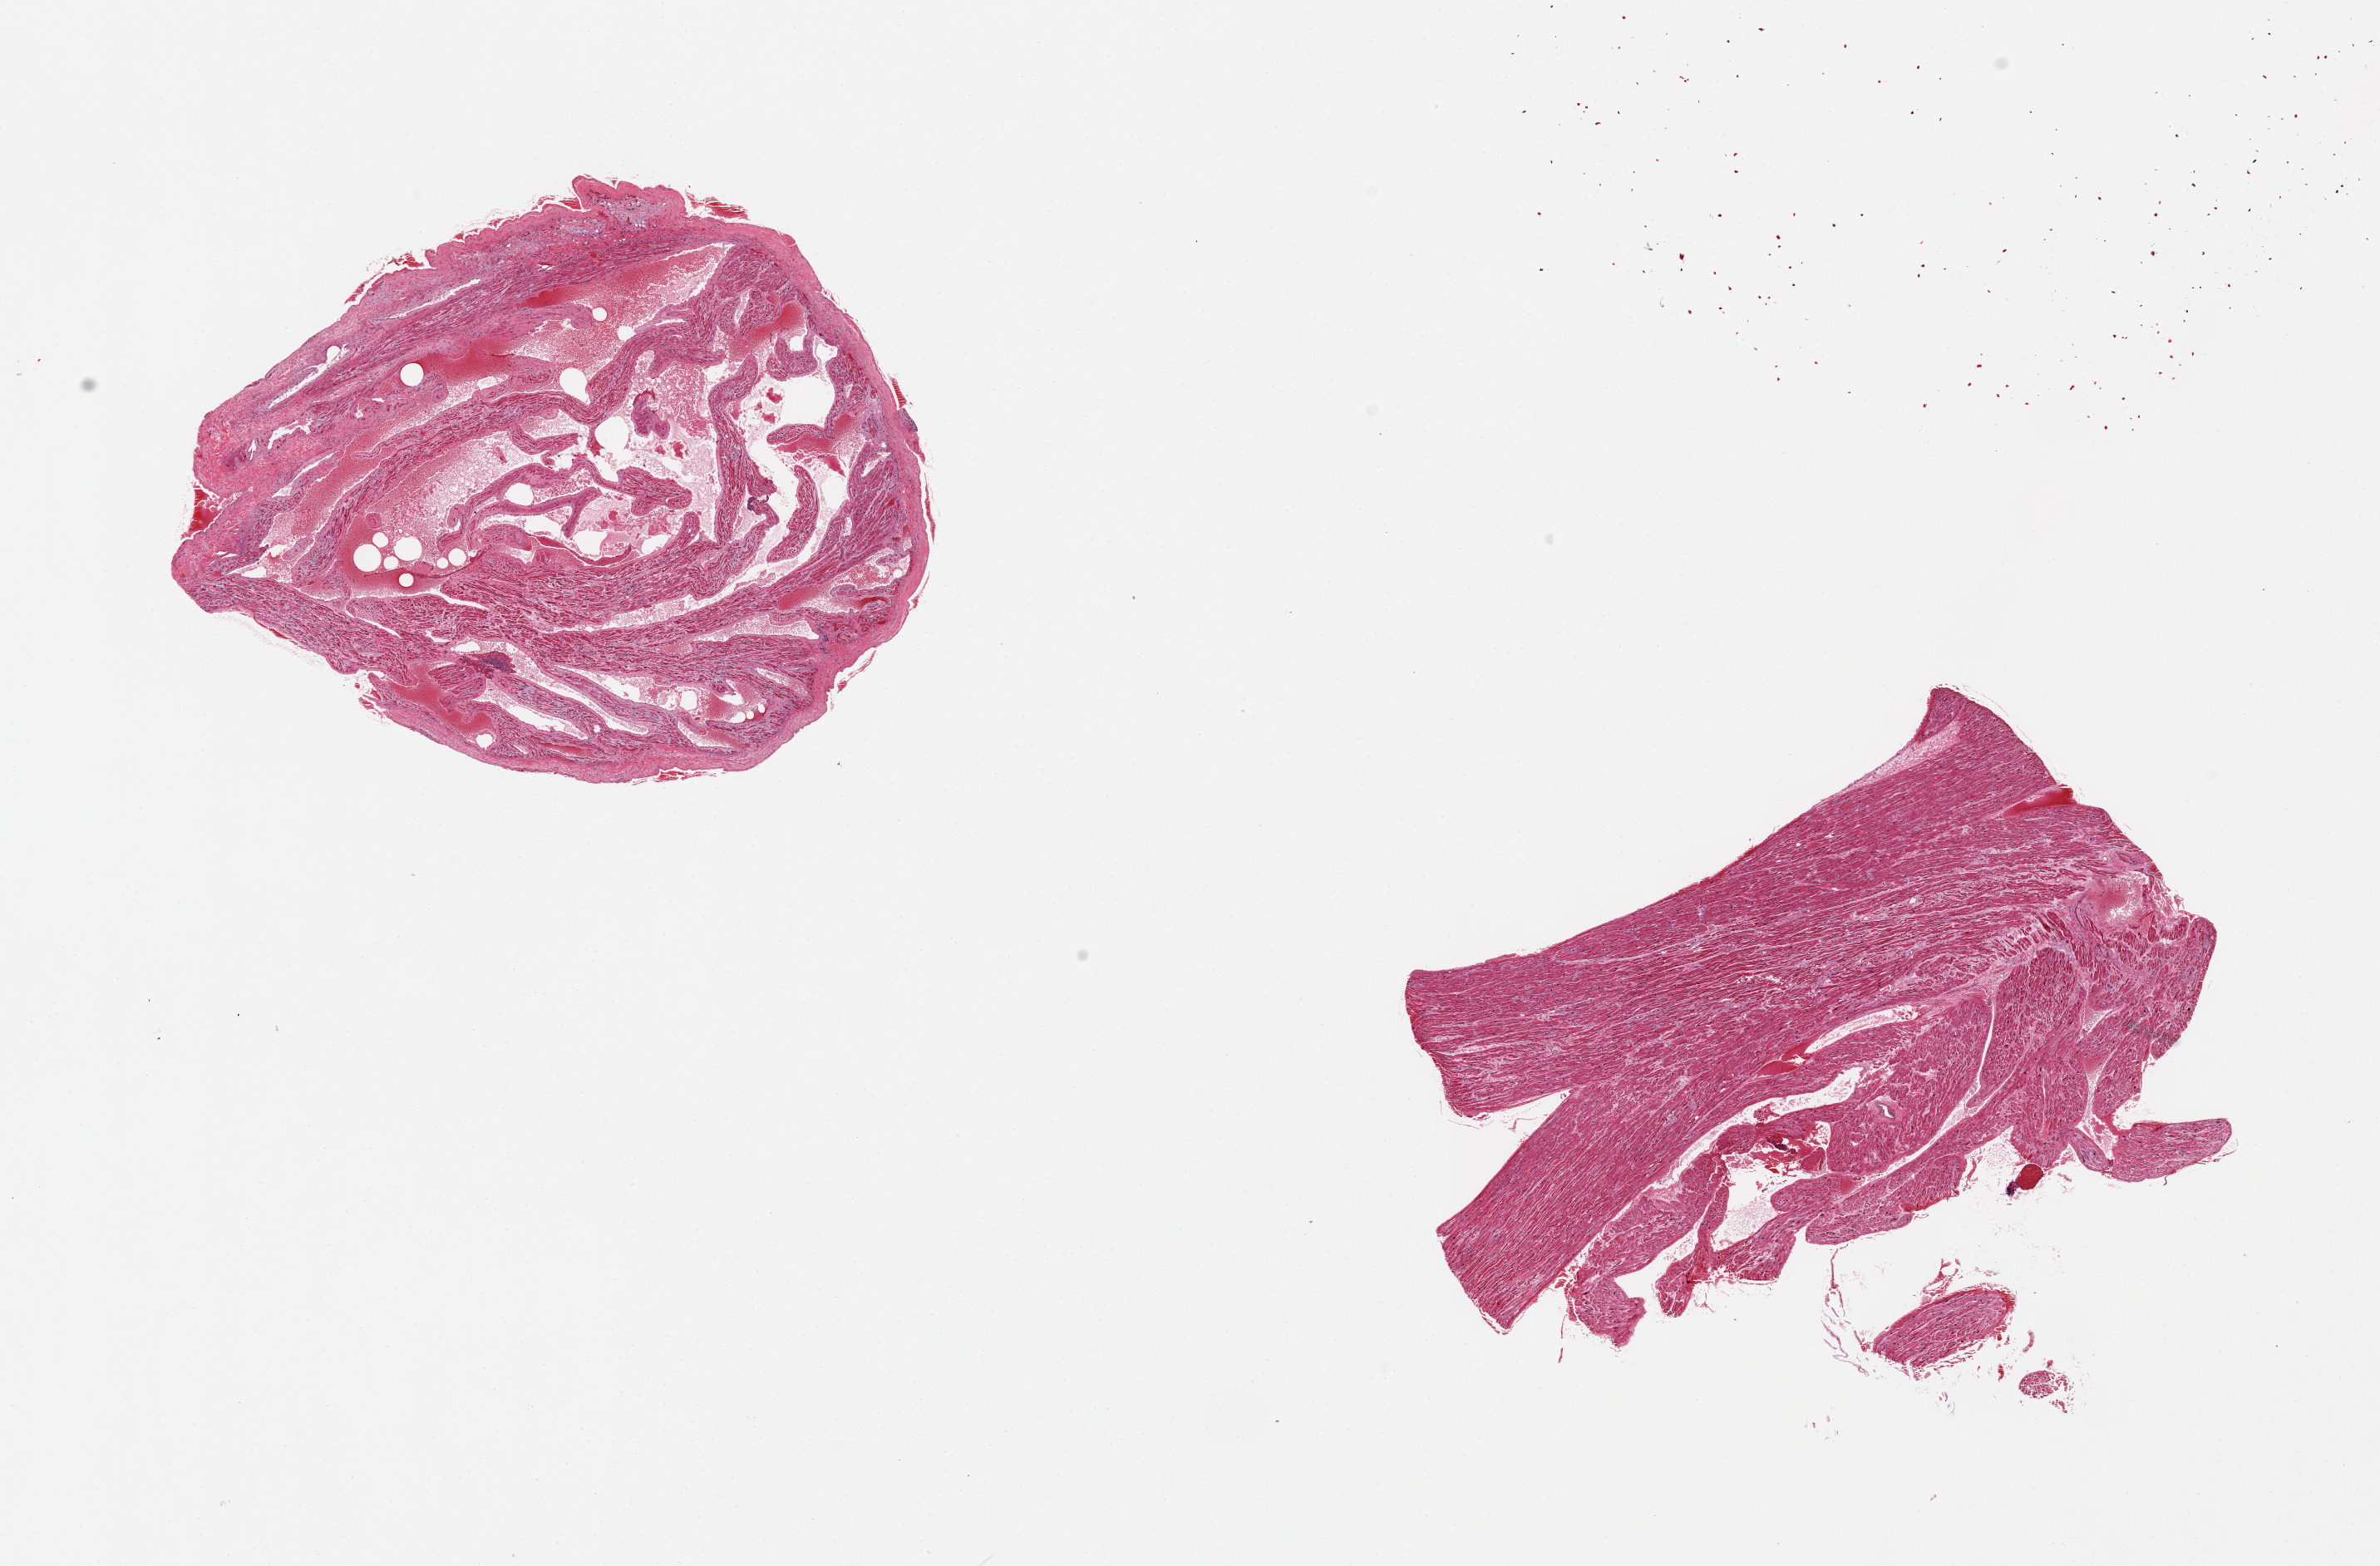
Whole-slide image, H&E stain, low-resolution overview of the scanned area, about 22.6 x 14.9 mm. PAXgene-fixed, paraffin-embedded tissue. Sampled site (target tissue): auricular appendage. Tissue donor sample.
Reviewer comment on this tissue sample: 2 pieces. Hypertrophied fibers.